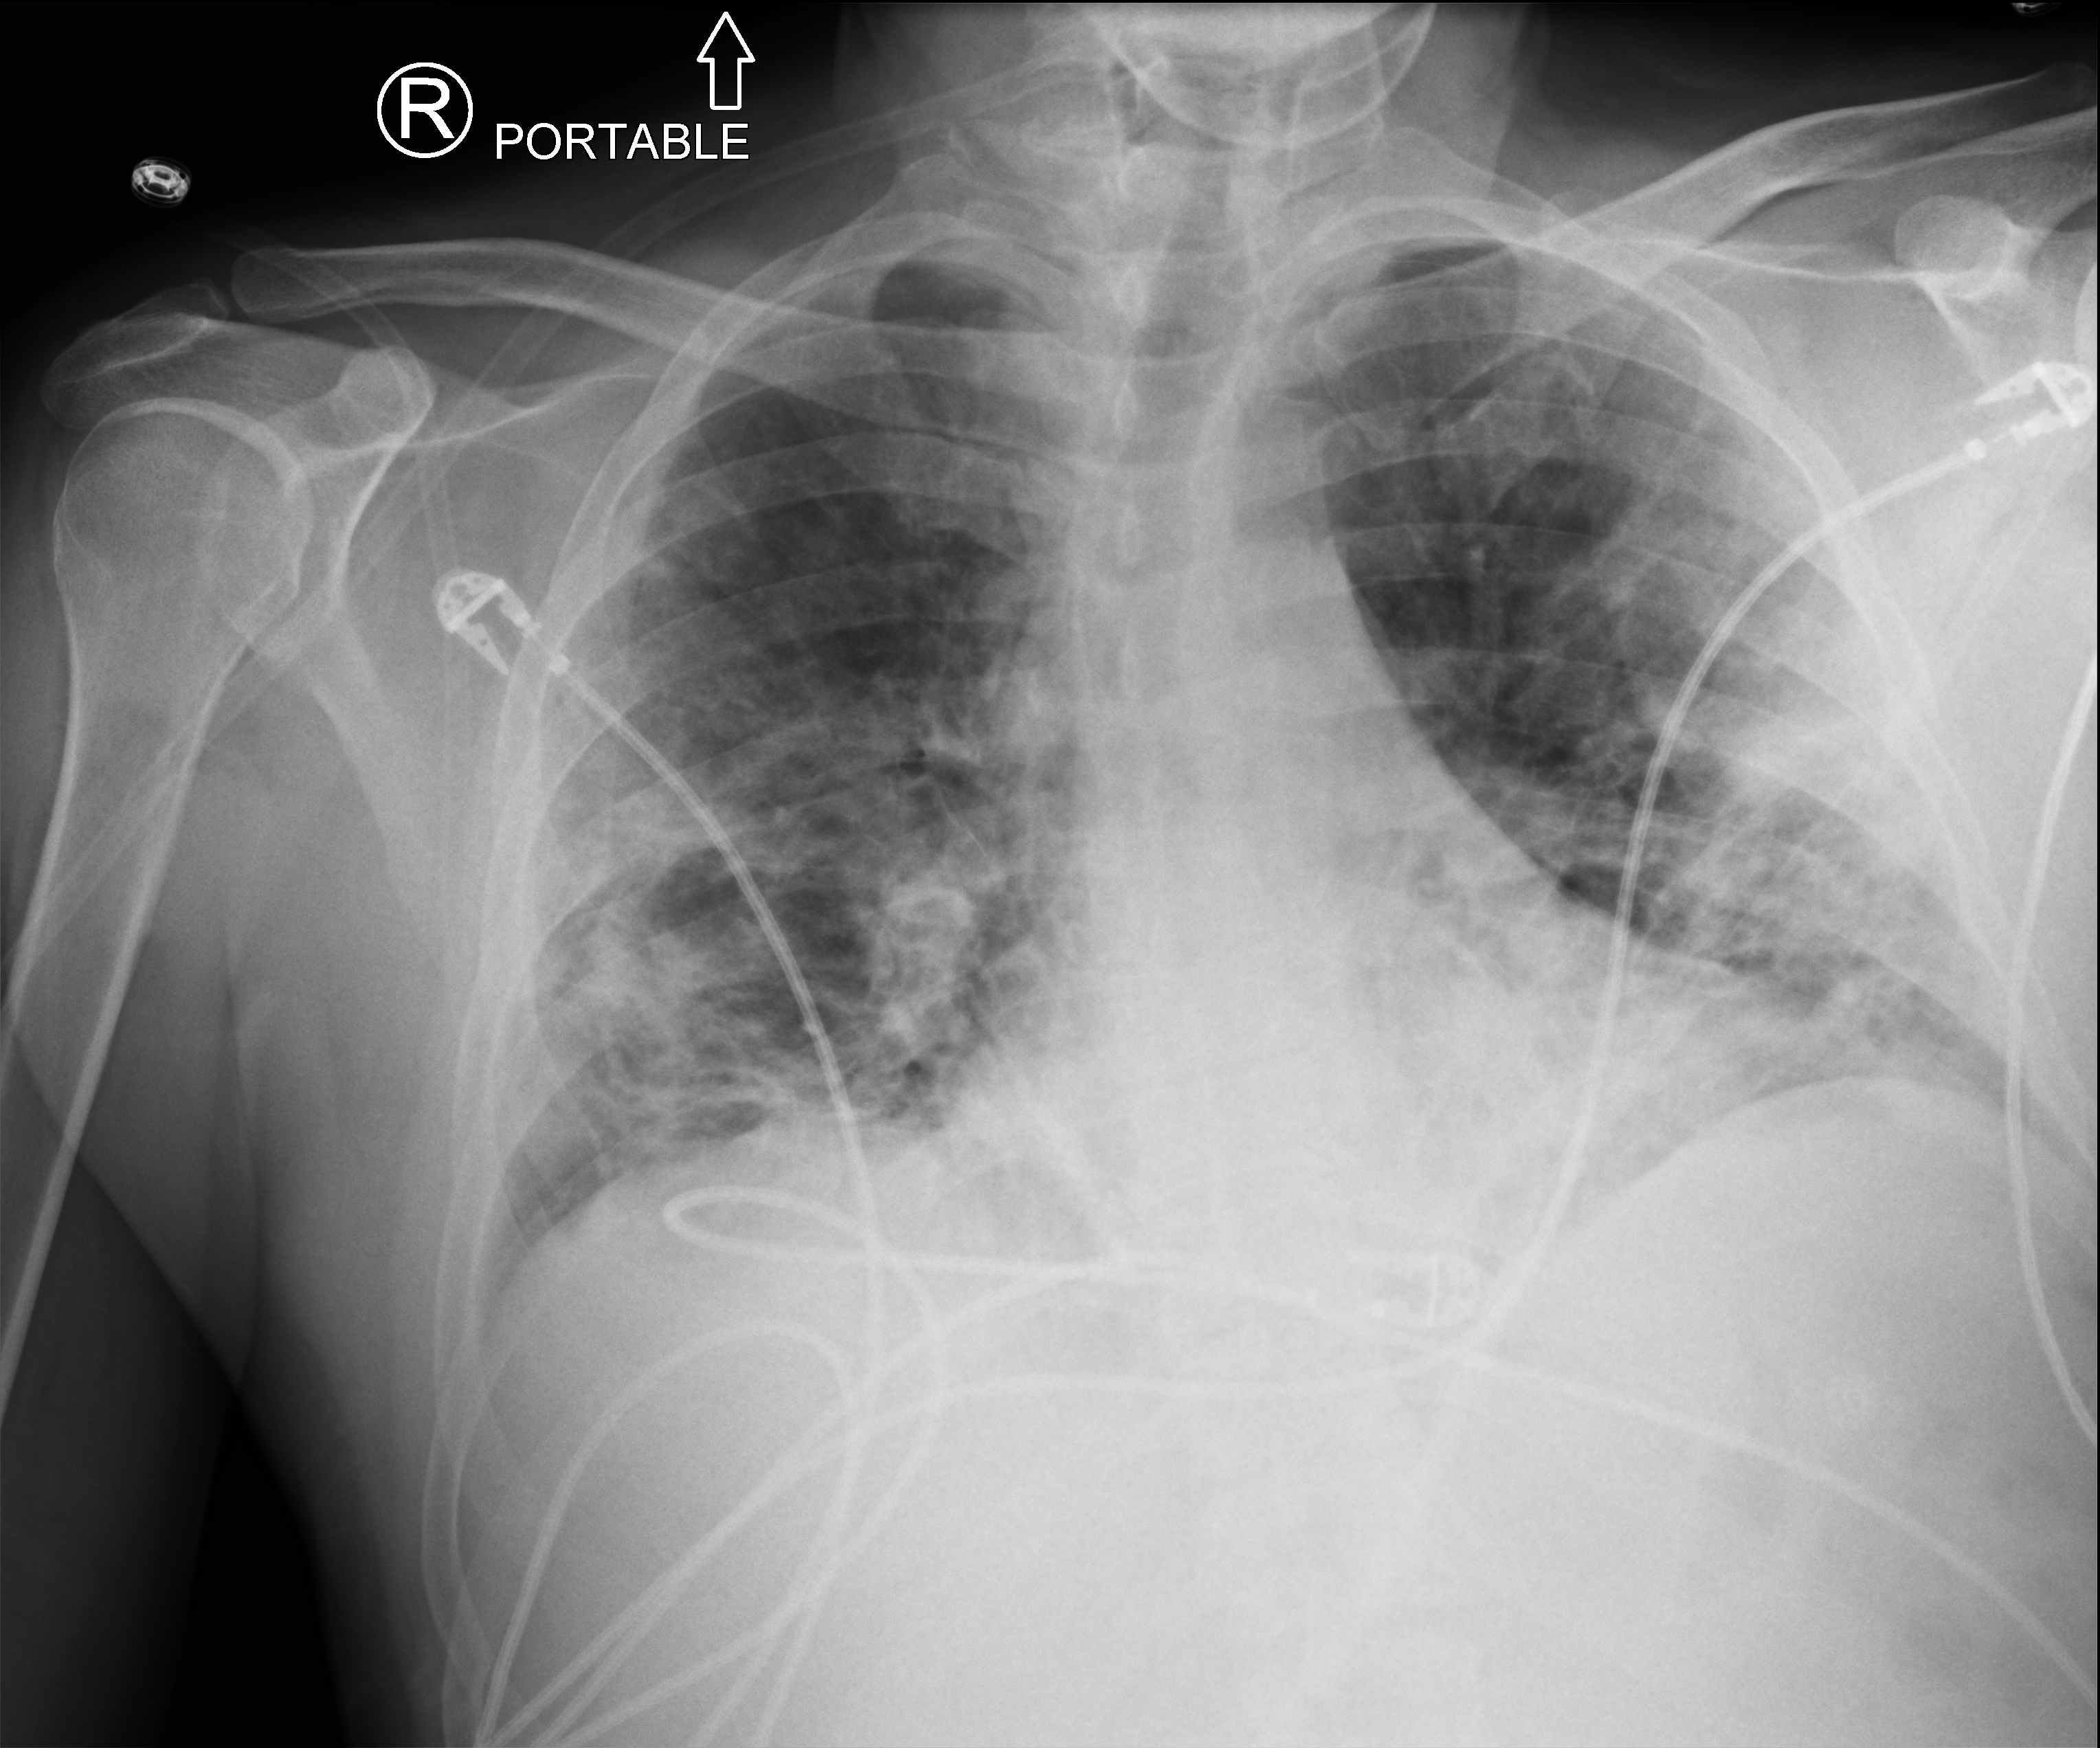
Bedside chest radiograph (computed radiography), anteroposterior (AP) projection. Patient hospitalised with COVID-19; male, aged 60–74 years.
From the hospital-stay record, not from the radiograph (when in the stay this image was taken is not recorded): other chronic lung disease (admission record): no.